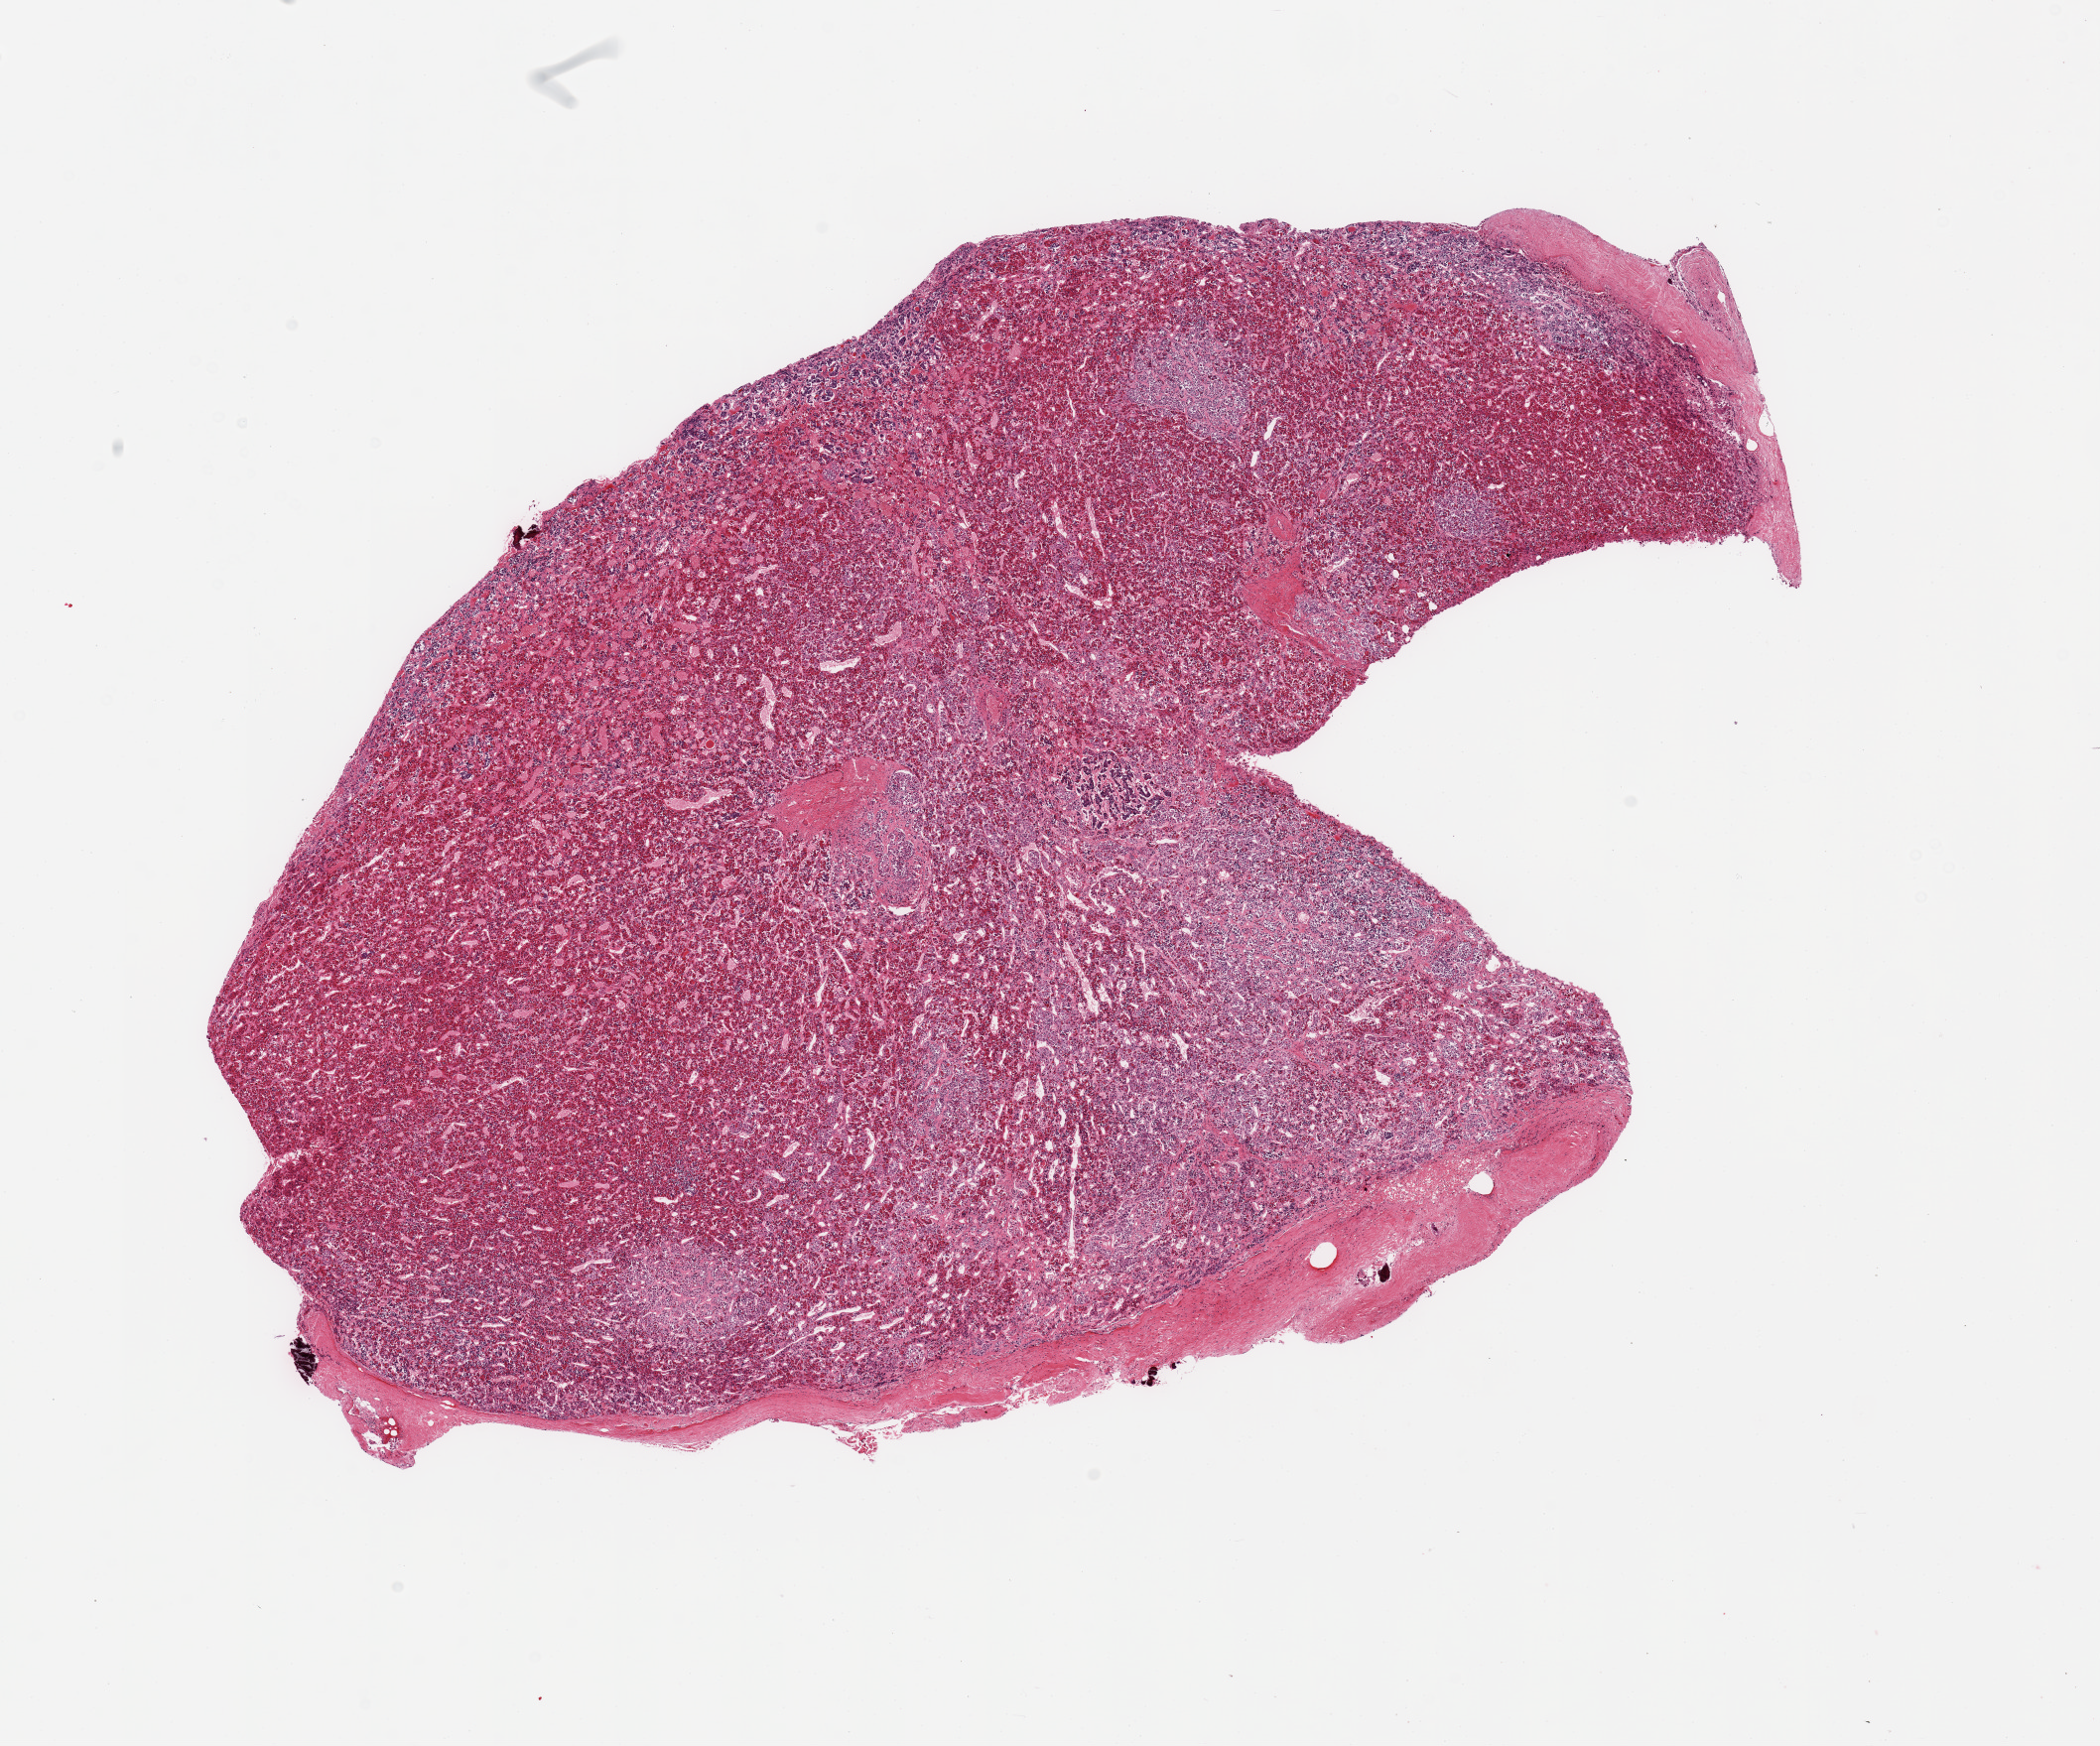
Hematoxylin and eosin (H&E) whole-slide image, brightfield — shown as a low-resolution overview of the whole scanned area (about 16.7 x 13.9 mm, slide scanned at 20x); PAXgene-fixed paraffin-embedded (PFPE) section; sampled site (target tissue): pituitary; donor tissue sample.
Pathologist's review note for this sample: 1 piece; all anterior lobe.